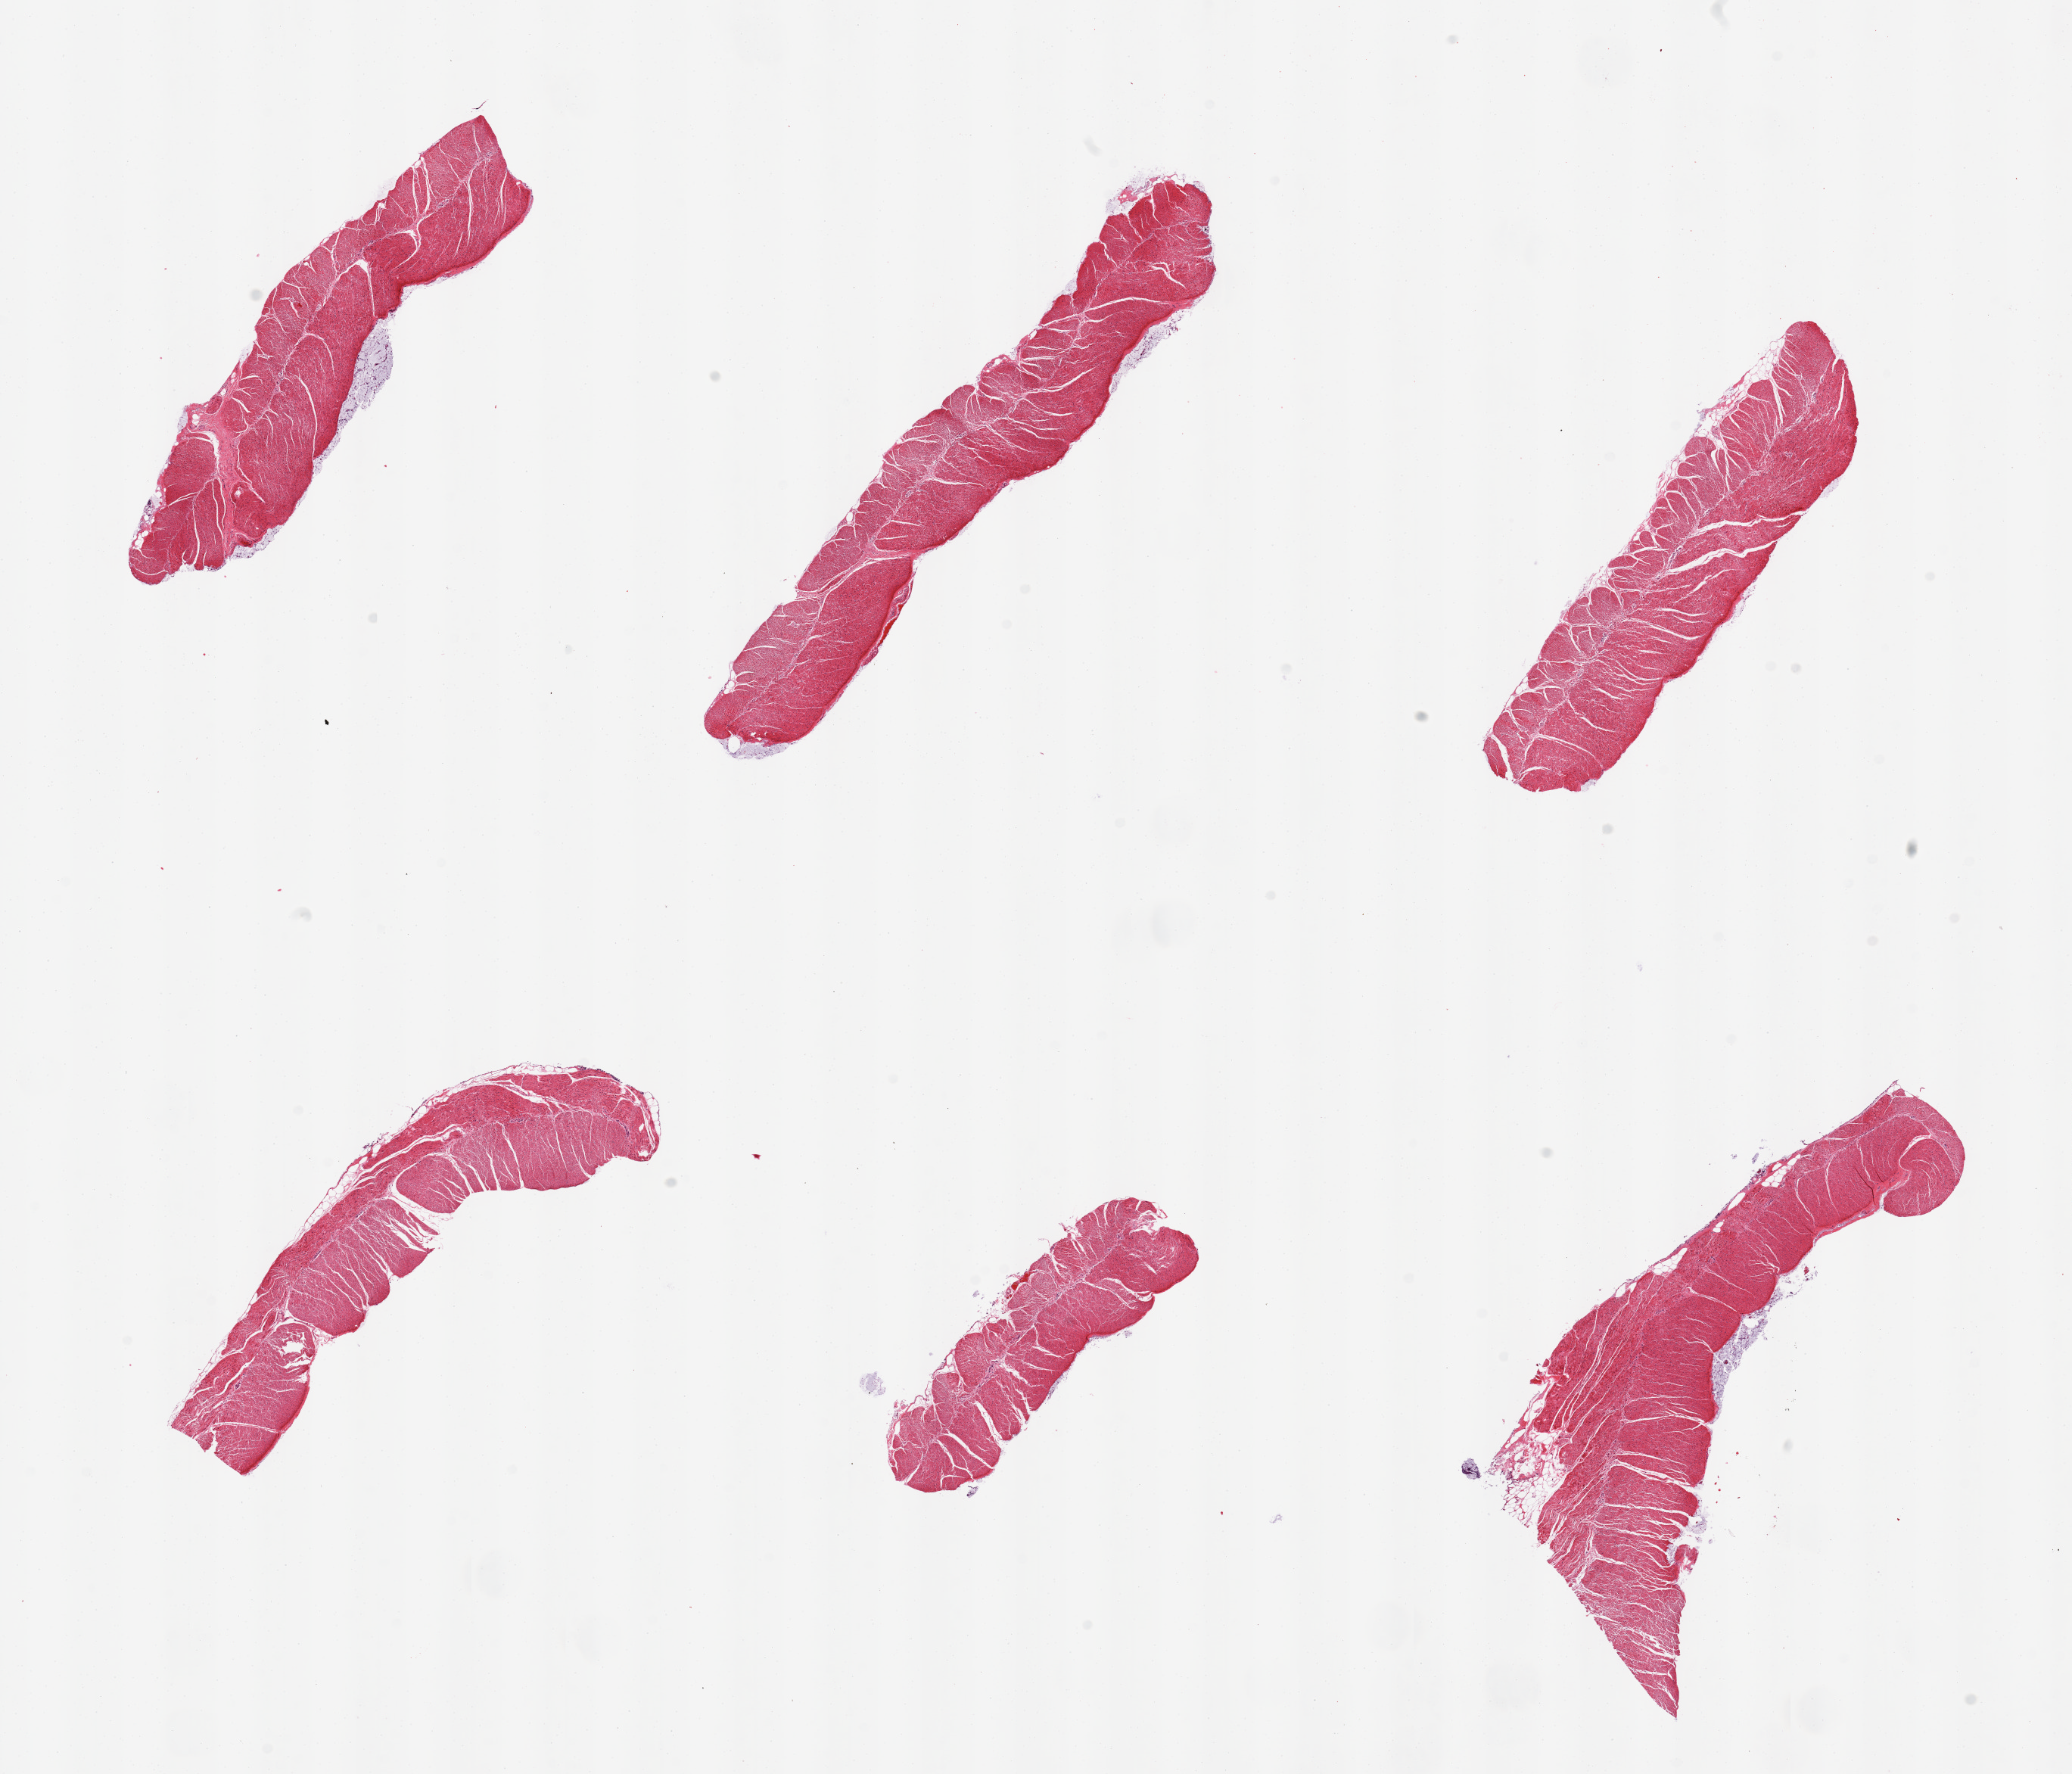
Whole-slide image, haematoxylin and eosin stain, brightfield — shown as a low-resolution overview of the whole scanned area (about 21.7 x 18.5 mm, acquisition: 20x scan). PAXgene-fixed paraffin-embedded (PFPE) section. Target tissue: sigmoid colon. Tissue donor sample. Donor sex: female.
Reviewer comment on this tissue sample: 6 pieces, well trimmed, residual cellular debris/mucus.